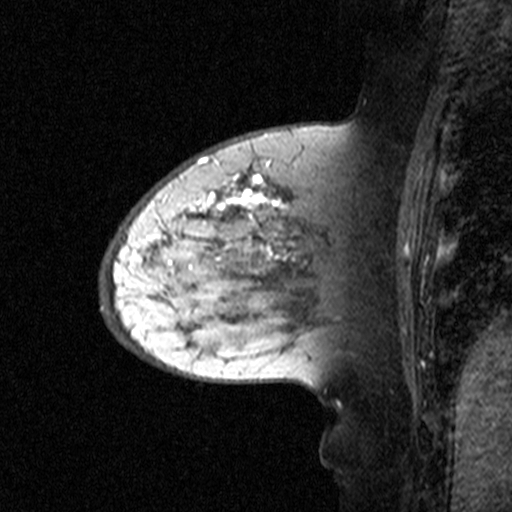
Breast MRI (dynamic contrast-enhanced), one sagittal slice. Slice 18 of 44 in the series (ordered by position). Dynamic contrast-enhanced study with each time point stored as its own series, time point 2 of 3 at this slice position (early post-contrast, ordered by acquisition time). 1.5 T. TE 4.5 ms, TR 11 ms. 512 × 512 image matrix, field of view 200 × 200 mm. Patient: female, 65 years. From the clinical record (not read from this slice): setting: breast cancer imaged before/during neoadjuvant chemotherapy; receptor status: HER2-positive.
Structures marked on this image (semi-automatic segmentation, software-assisted and operator-edited):
- analysis volume of interest (the breast-tissue region the enhancement analysis was run in; not a lesion): bounding box <160,172,329,345> (left, top, right, bottom; pixels)
- tumour enhancement mask (voxels above the 90 % enhancement threshold inside the analysis volume of interest): <164,174,291,261>